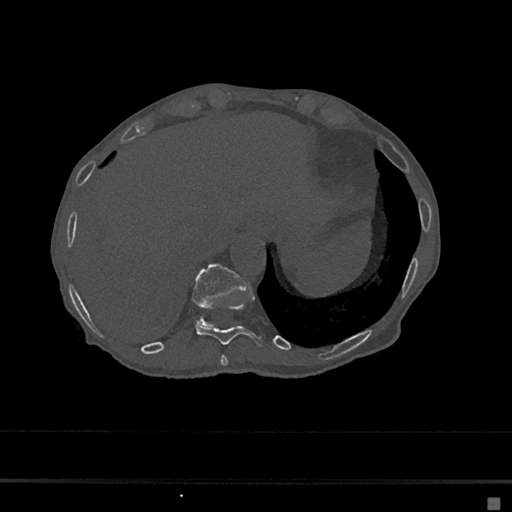
CT including the spine, one axial slice. Position 212 of 797 along the scan axis. Reconstruction kernel Br40s/3. Bone window (W 1800 / L 400 HU). 0.5 mm slice thickness. 512 × 512 image matrix, field of view 360 × 360 mm. Patient: female, 68 years. Case-level facts recorded for this patient, not image findings: primary cancer: renal.
Structures marked on this image (semi-automatic segmentation, software-assisted and operator-edited):
- T10 vertebra: box from (x=195, y=303) to (x=263, y=347) px
- T11 vertebra: (x=192, y=263)–(x=248, y=326)
- T9 vertebra: (x=220, y=355)–(x=228, y=366)